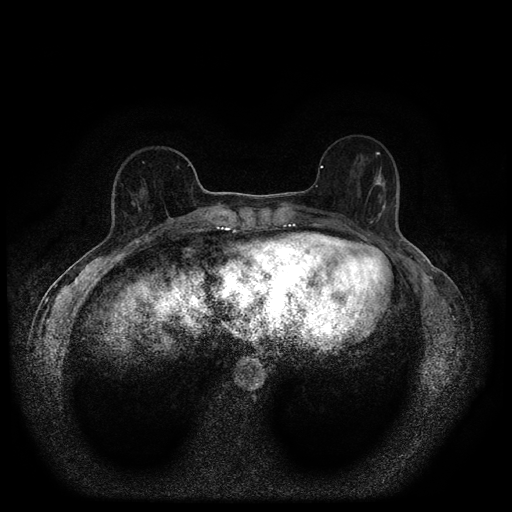
Breast MRI (dynamic contrast-enhanced, multi-phase), one axial slice; slice 34 of 116 in the series (ordered by position); dynamic contrast-enhanced series, time point 2 of 5 at this slice position (early post-contrast); 1.5 T; TE 2.7 ms, TR 5.4 ms; 512 × 512 image matrix, field of view 330 × 330 mm. Patient: female, 56 years.
Annotated regions visible in this slice (semi-automatic segmentation, software-assisted and operator-edited):
- breast lesion (labelled 'tumour' in the annotation; benign lesions carry a separate 'benign' label): bounding box (x1, y1, x2, y2) in pixels: (369, 166, 386, 193)